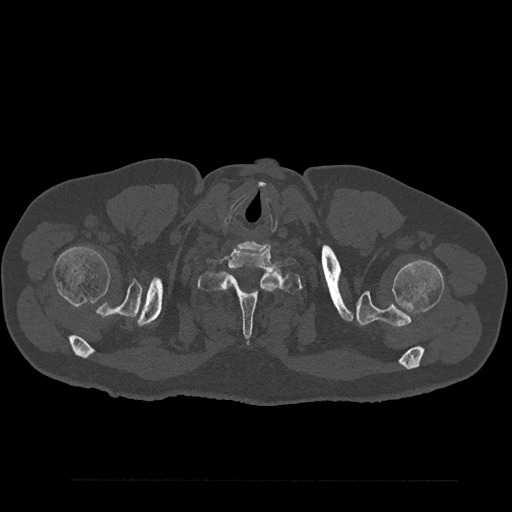
CT including the spine, one axial slice; slice 765 of 797 in the series (ordered by position); reconstruction kernel Br40s/3; 120 kVp; bone window (W 1800 / L 400 HU); 0.5 mm slice thickness; 512 × 512 image matrix, field of view 430 × 430 mm. Male patient, age 61 years. From the clinical record (not read from this slice): primary cancer: prostate.
Outlined on this slice (semi-automatic segmentation, software-assisted and operator-edited):
- T1 vertebra: bounding box <198,261,302,337> (left, top, right, bottom; pixels)